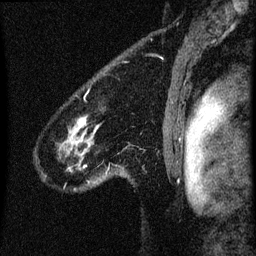
Breast MRI (dynamic contrast-enhanced), one sagittal slice. Position 54 of 60 along the scan axis. Dynamic contrast-enhanced series, image 2 of 3 at this slice position (ordered by acquisition). 1.5 T. TE 4.2 ms, TR 8 ms. 256 × 256 image matrix, field of view 180 × 180 mm. Patient: female, 61 years.
Outlined on this slice (semi-automatically segmented with operator editing):
- analysis volume of interest (the breast-tissue region the enhancement analysis was run in; not a lesion): box from (x=45, y=116) to (x=108, y=189) px
- tumour enhancement mask (voxels above the 70 % enhancement threshold inside the analysis volume of interest): (x=81, y=120)–(x=83, y=123)